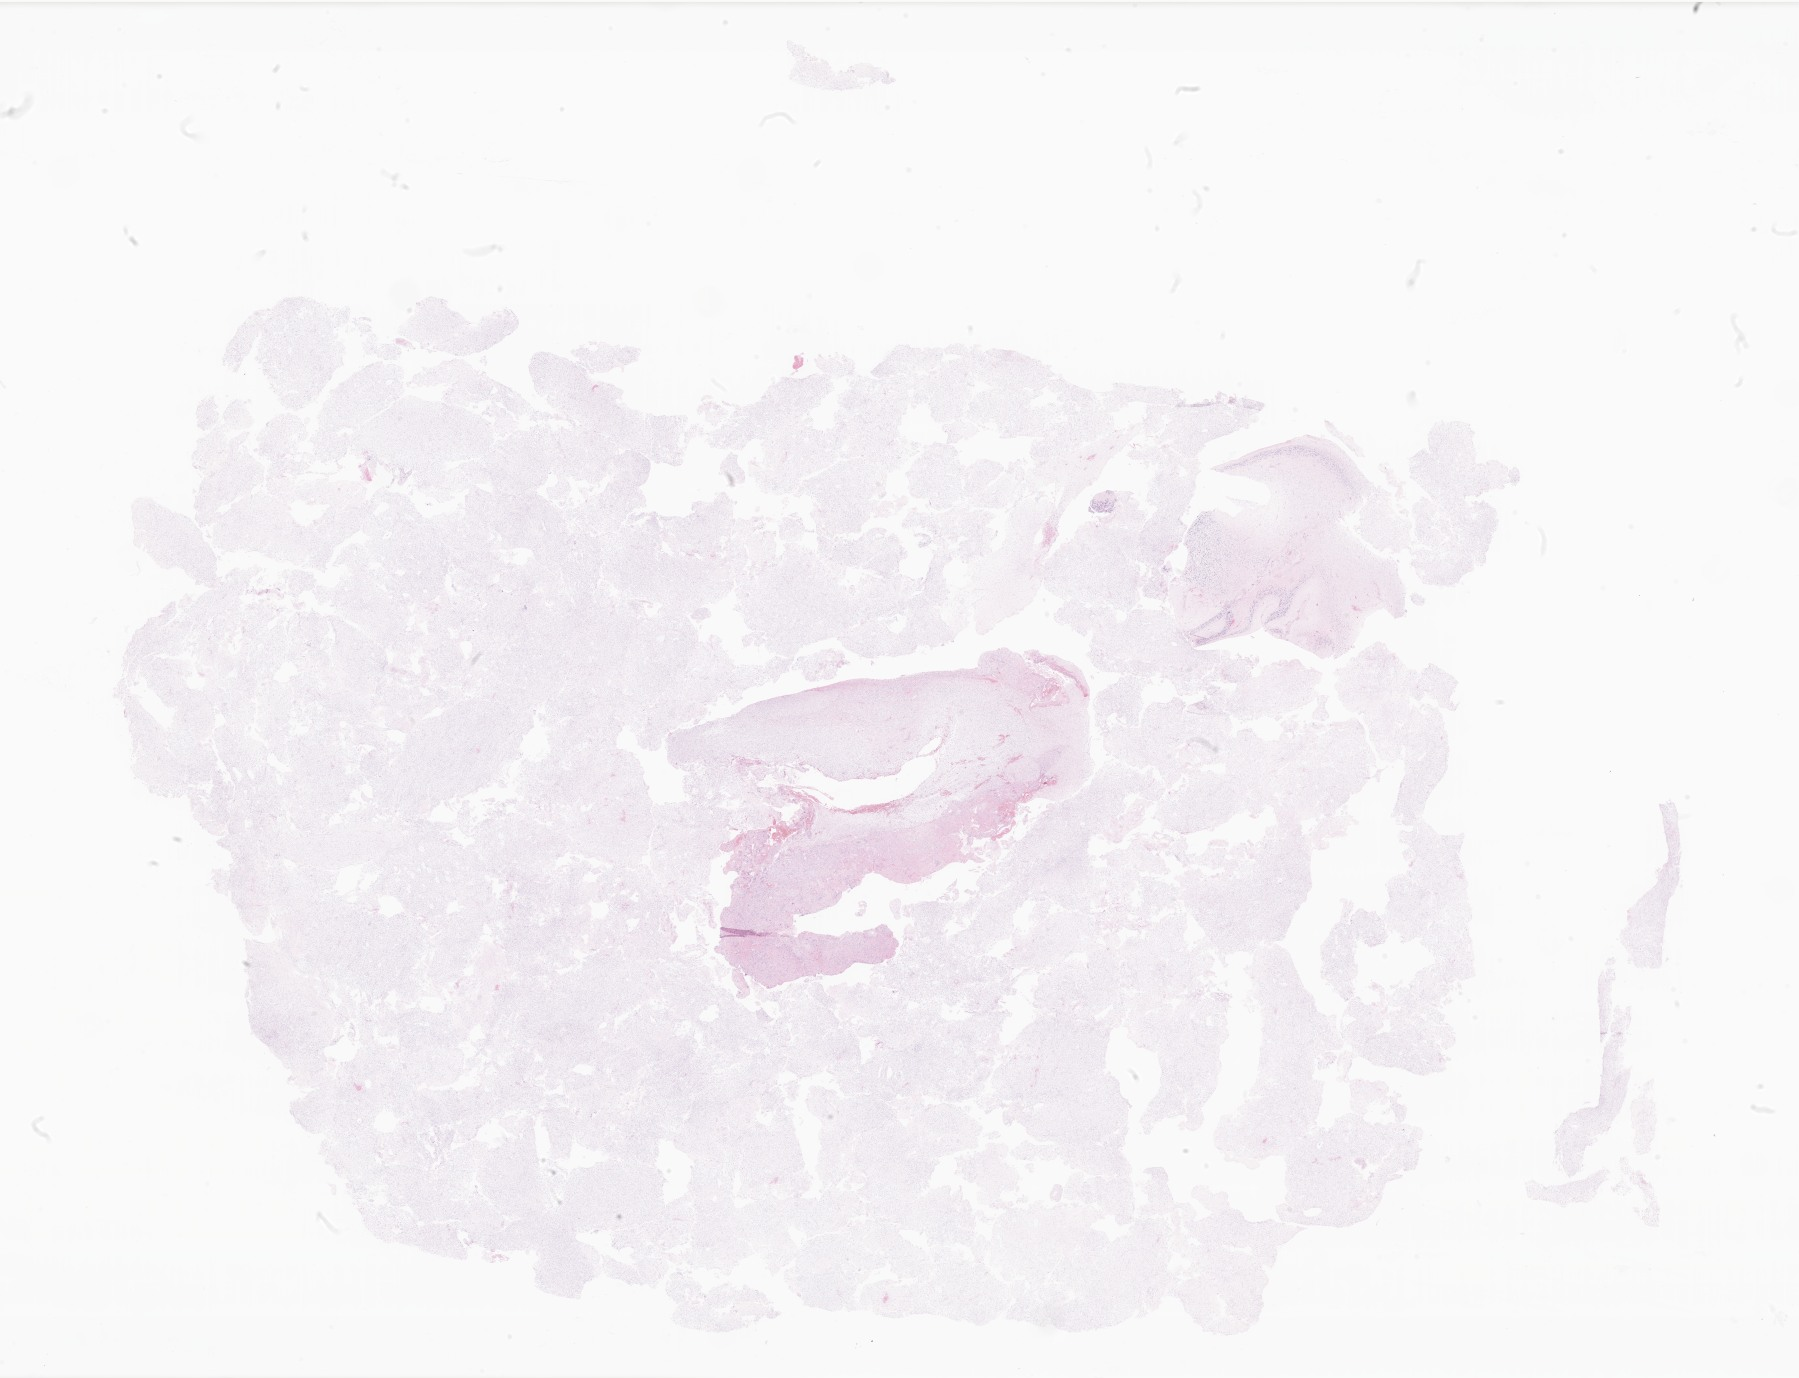
Whole-slide image, haematoxylin and eosin stain of tumor tissue from the brain — low-resolution overview of the scanned area, about 30.3 x 23.2 mm. FFPE section. Female patient, age 95 months (7 years 11 months).
Recorded diagnosis: Pilocytic astrocytoma.